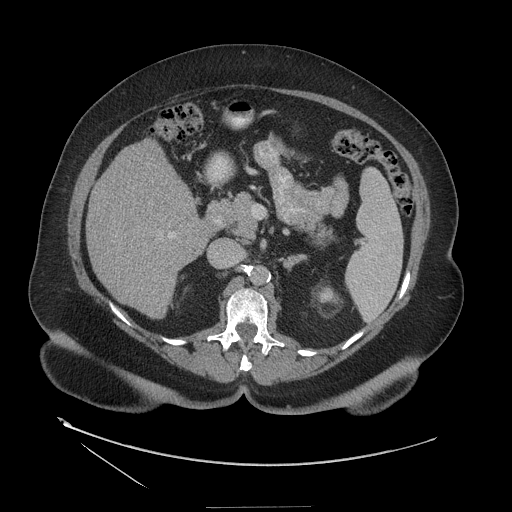
Contrast-enhanced abdominal CT (liver protocol), one axial slice; position 62 of 127 along the scan axis; 140 kVp; soft-tissue window (W 400 / L 40 HU); 2.5 mm slice thickness; 512 × 512 image matrix, field of view 480 × 480 mm. Case-level facts recorded for this patient, not image findings: diagnosis: hepatocellular carcinoma (patient treated with transarterial chemoembolisation; whether this scan precedes or follows treatment is not stated here); TNM stage (as recorded): Stage-II; Child-Pugh class: A; tumour differentiation: well differentiated; tumour nodularity: multinodular.
Annotated regions visible in this slice (semi-automatically segmented with operator editing):
- liver parenchyma outside the tumour (the mass and vessels are separate outlines, so this box may not span the whole liver): bounding box [x1, y1, x2, y2] px = [86, 140, 210, 318]
- liver vessels: [169, 235, 172, 238]